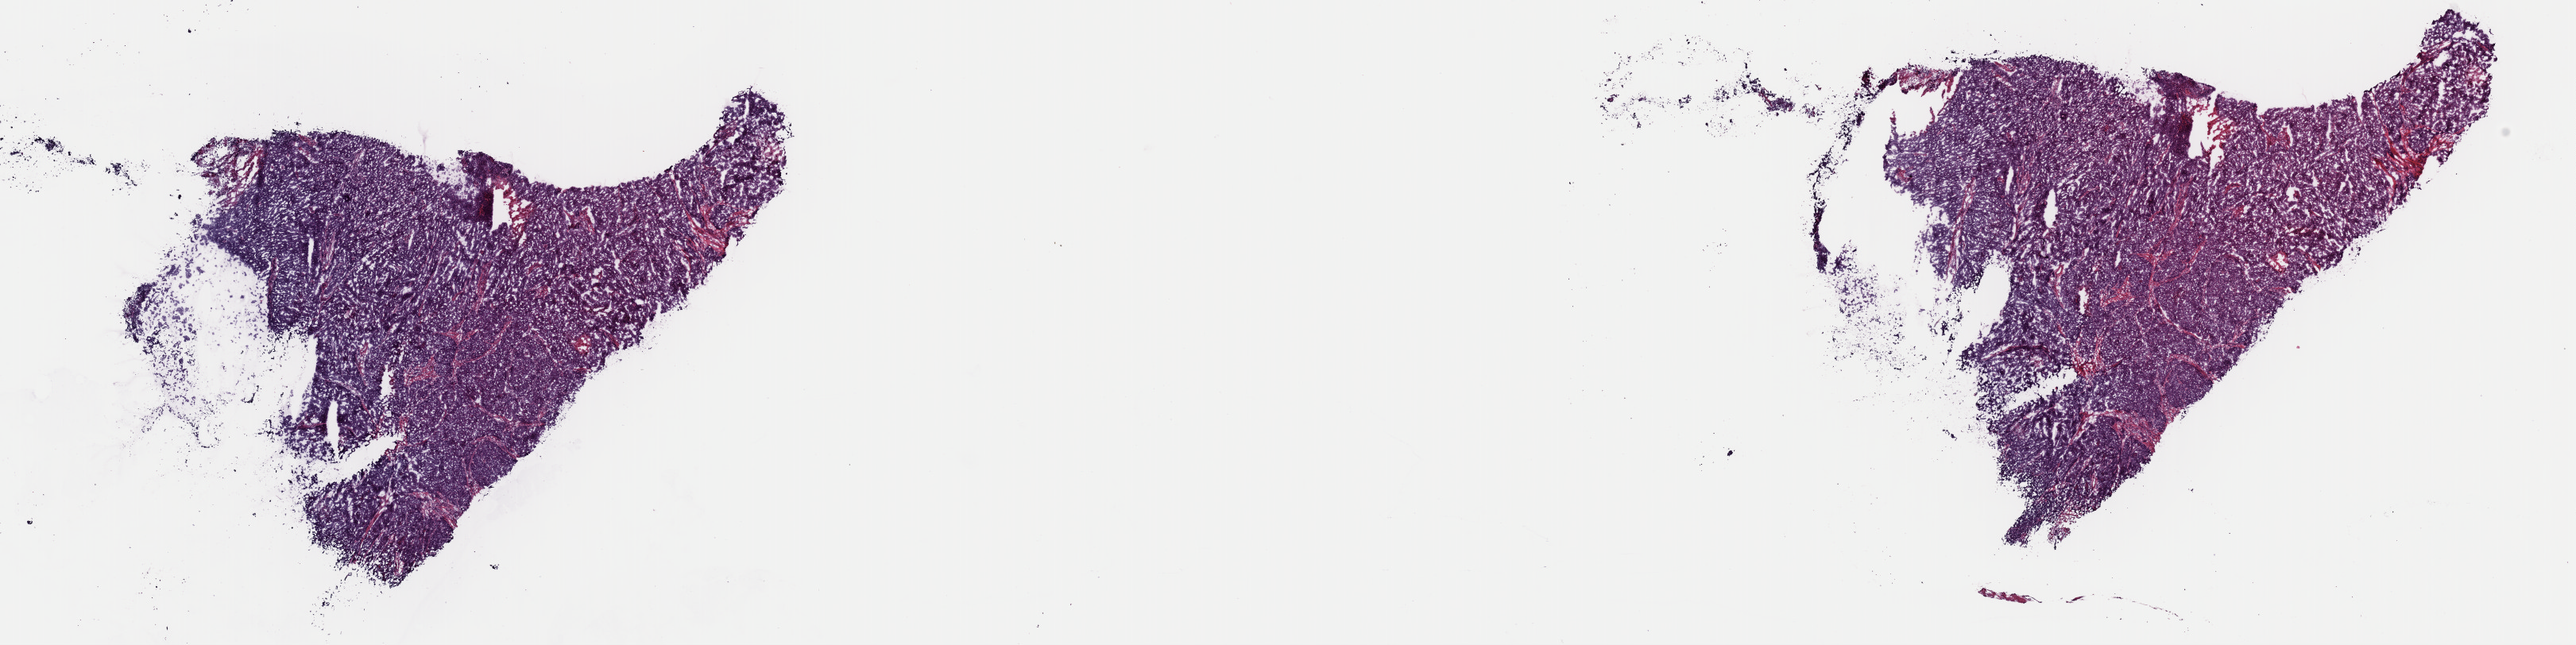
Digitized H&E-stained tissue section (whole slide), whole scanned area (about 25.6 x 6.4 mm, acquisition: 40x scan) shown as a low-resolution overview, frozen section, primary tumour sample from the cervix. Patient: female, age at initial diagnosis 30 years. Histologic grade: G3 (poorly differentiated). Composition of this section per pathologist review: tumour cells 80%, tumour nuclei 80%, normal cells 0%, stromal cells 20%, necrosis 0%. Infiltration values recorded for this section: lymphocyte infiltration 40%, monocyte infiltration 20%, neutrophil infiltration 20%.
• FIGO stage: IIIB
• pathologic diagnosis: Adenocarcinoma, endocervical type (cervix uteri)